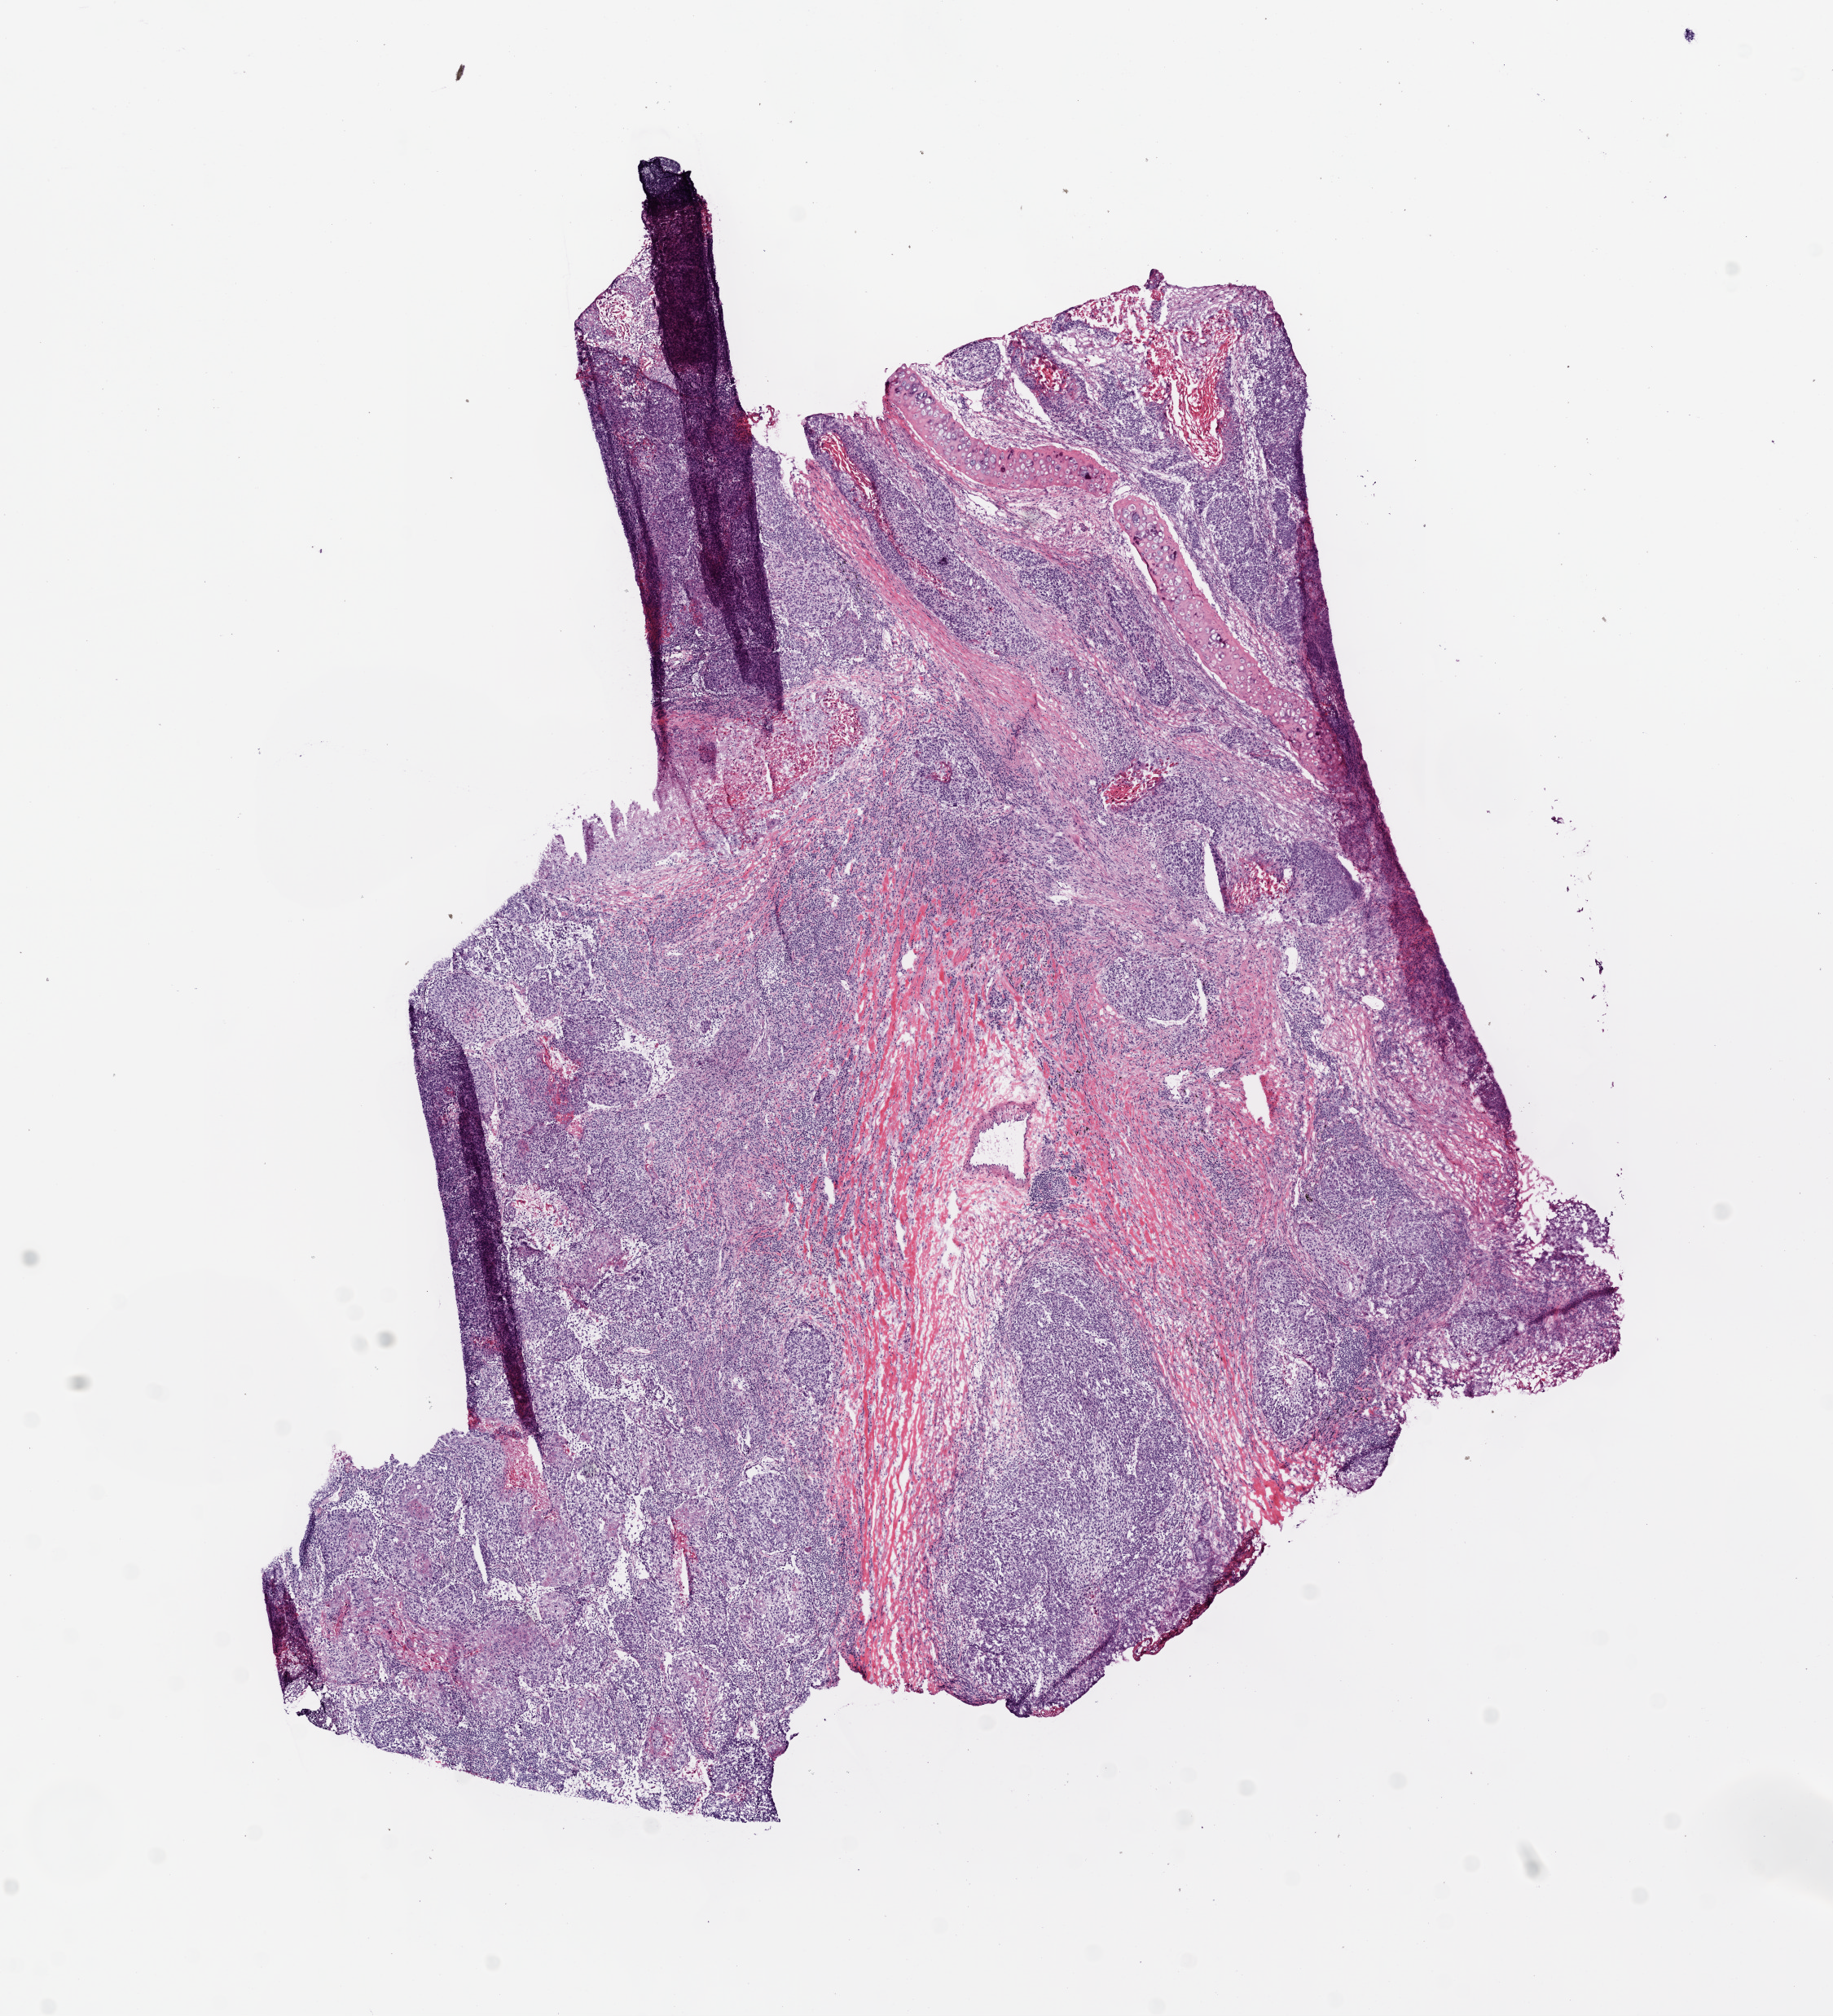
H&E-stained whole-slide image — a low-resolution overview of the entire scanned area, about 9.0 x 9.9 mm; frozen section; sample: primary tumour, lung. Male, age 62 years at initial diagnosis. Pathologist review of this section (percent, as recorded): tumour cells 78%, tumour nuclei 70%, normal cells 5%, stromal cells 10%, necrosis 7%.
- pathologic diagnosis: Squamous cell carcinoma, NOS (lower lobe, lung)
- AJCC pathologic stage: IIIB (6th edition)